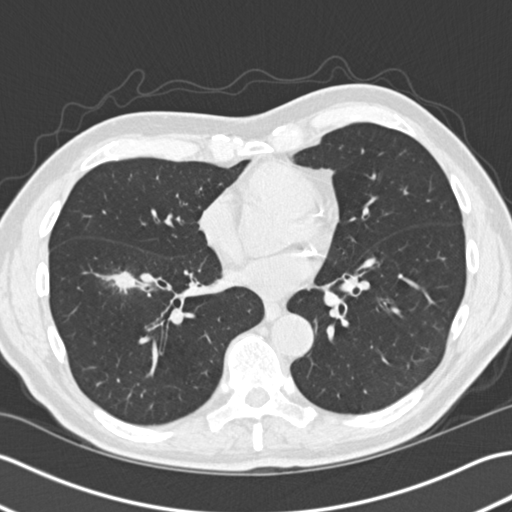
Low-dose screening chest CT, one axial slice. Slice 72 of 172 in the series (ordered by position). Reconstruction kernel B30f. Lung window (W 1500 / L -600 HU). 2 mm slice thickness. 512 × 512 image matrix, field of view 350 × 350 mm.
Annotated regions visible in this slice (expert manual segmentation):
- lesion 1 (tumor, lower lobe of right lung): bounding box (x1, y1, x2, y2) in pixels: (103, 271, 154, 297)